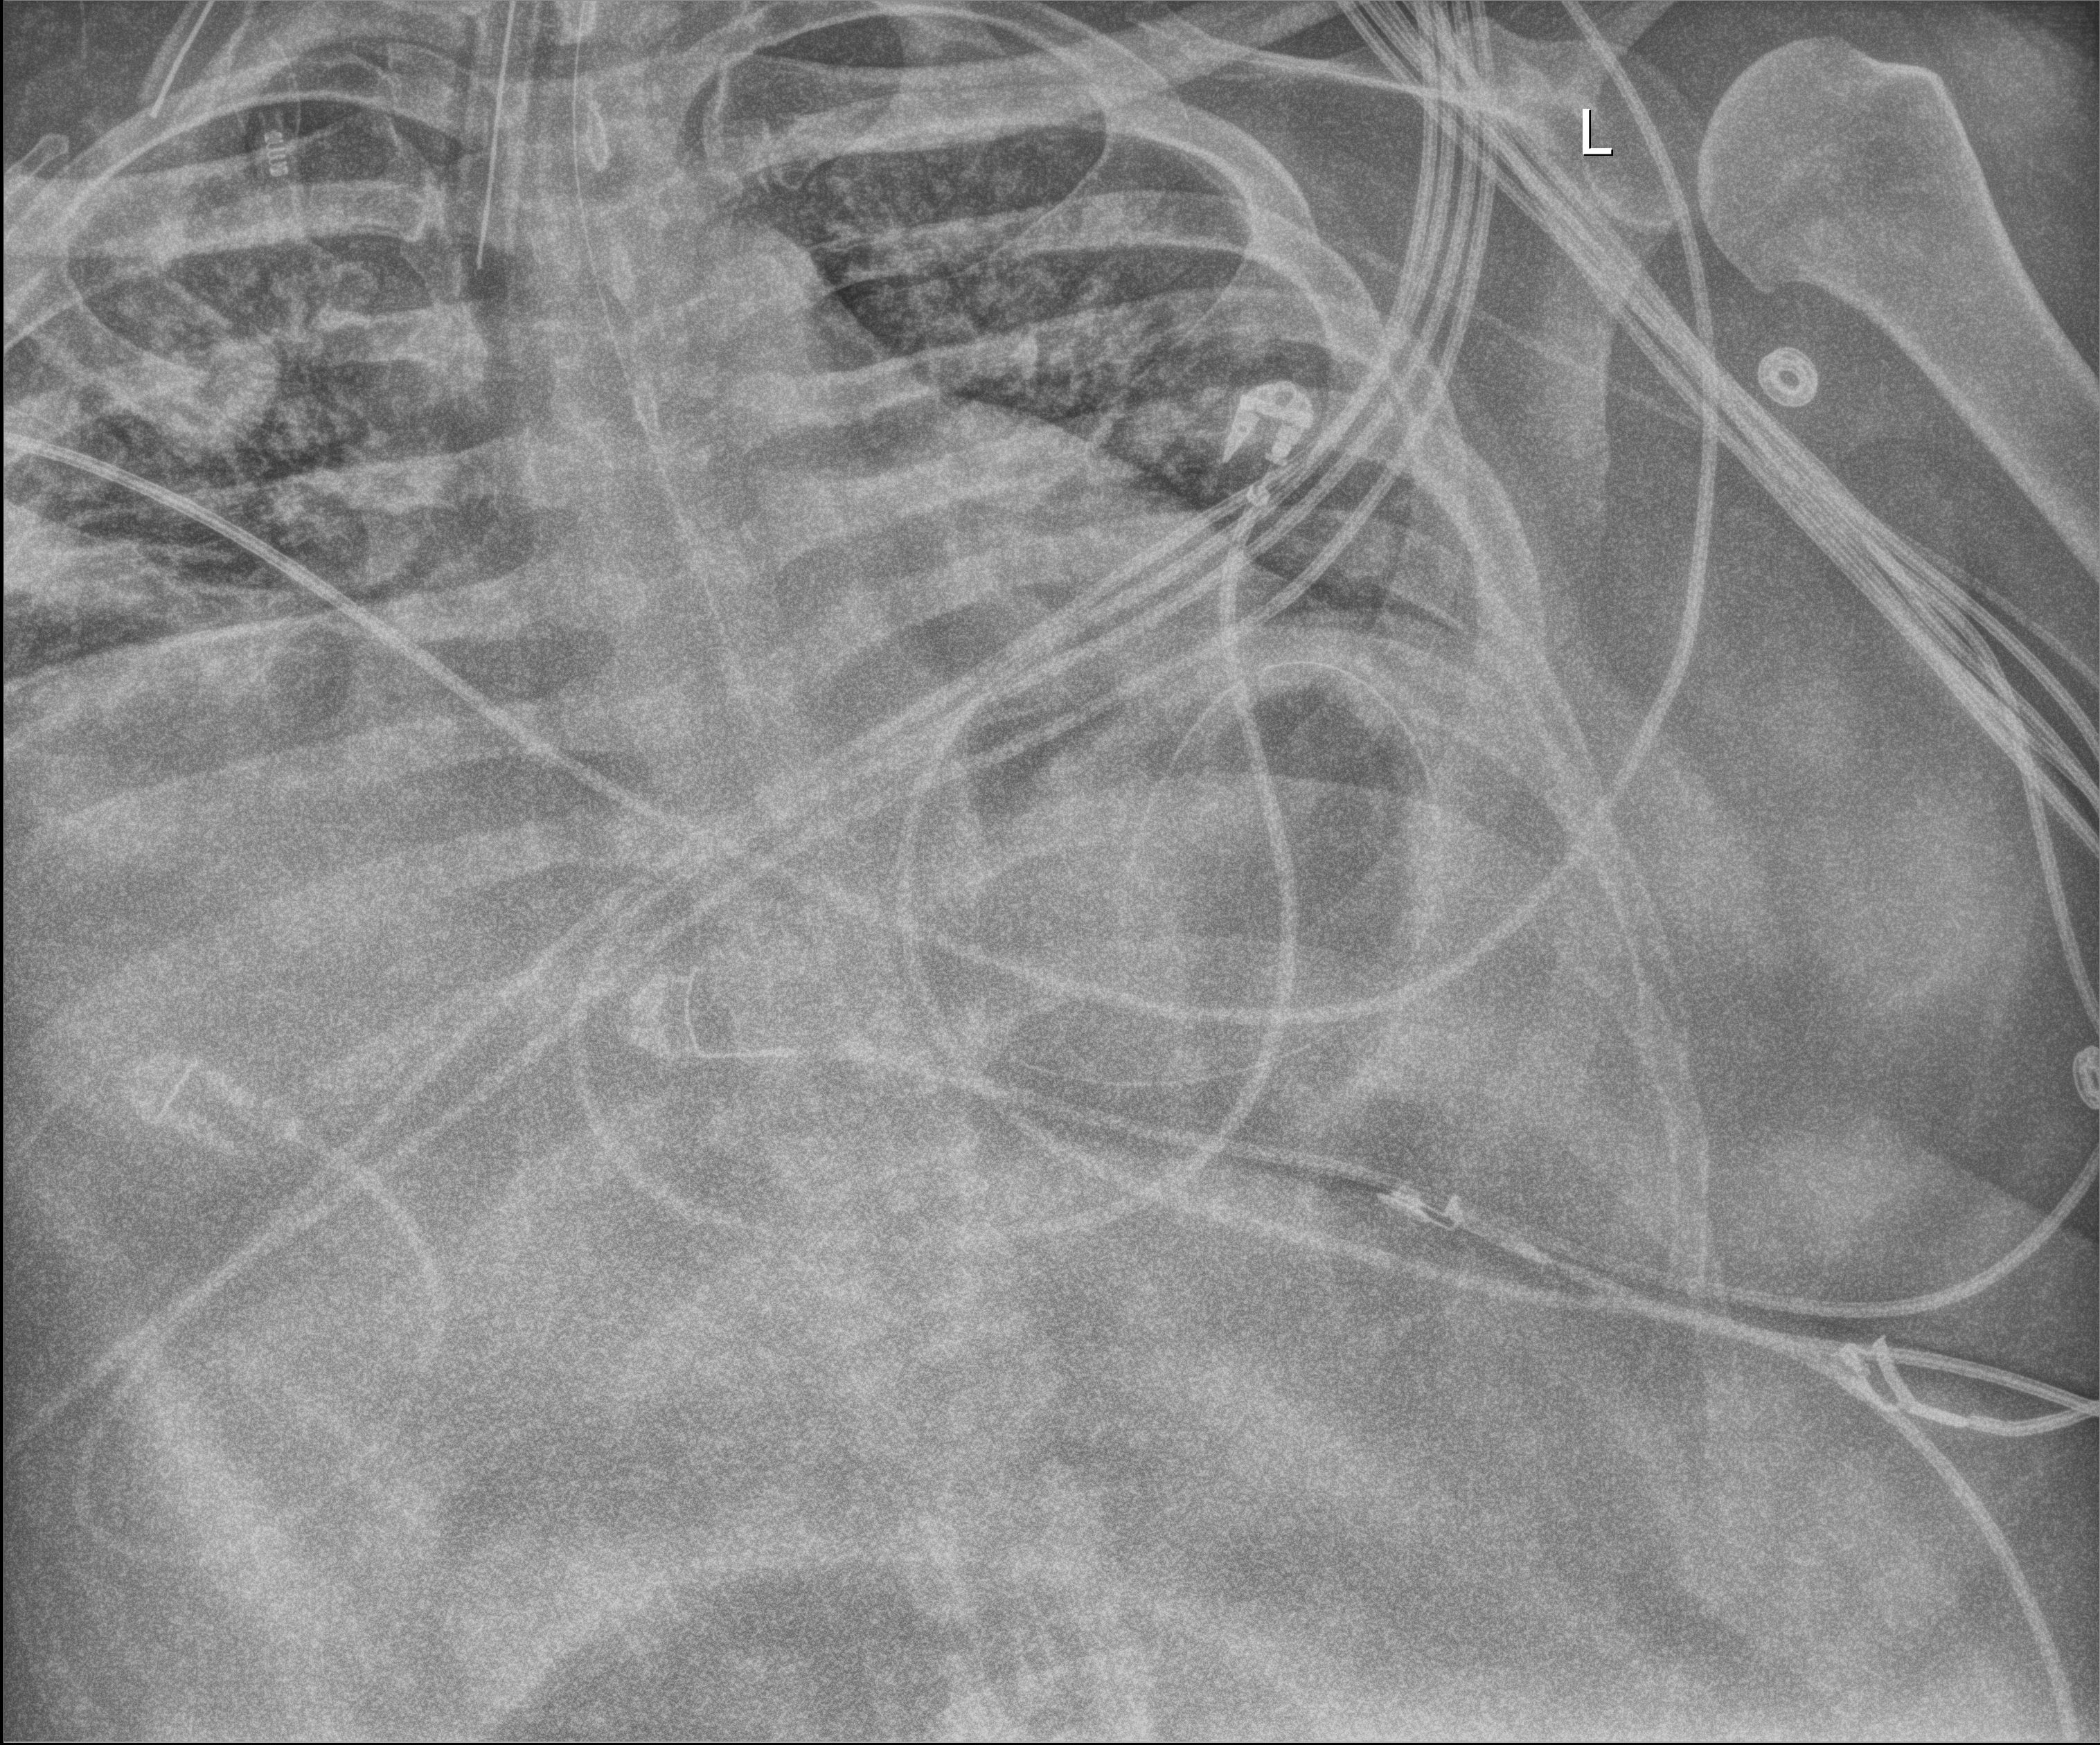
Chest radiograph; anteroposterior (AP) projection. Patient hospitalised with COVID-19; male, aged 18–59 years.
Admission-level facts for this patient (not findings on this image; timing relative to this image not recorded): mechanically ventilated during this hospital stay: yes; length of hospital stay: 69 days.